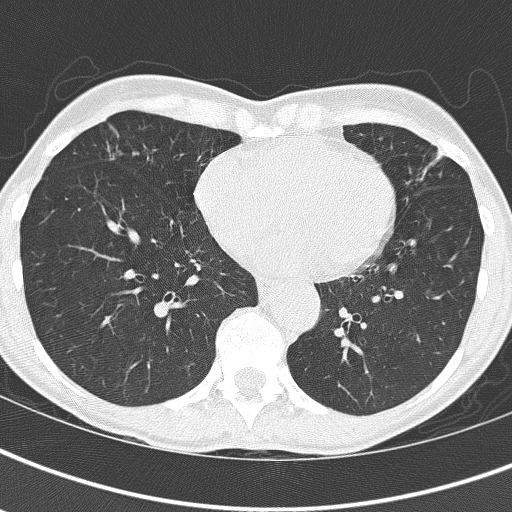
Axial slice from a low-dose chest CT screening exam; first (baseline) screen; lung window (W 1500 / L -600 HU); 2 mm slice thickness; slice 103 of 161 in the series. Female participant, aged 67 years at enrolment. Current smoker at enrolment.
- Lesion marked by an expert reader, bounding box [x1, y1, x2, y2] px = [81, 115, 180, 199].
- No non-calcified nodule or mass ≥4 mm was recorded by the screening reader at this exam.
- Official screen result: negative screen, significant abnormalities not suspicious for lung cancer.
- Later outcome: lung cancer diagnosed 832 days after this screen — bronchiolo-alveolar adenocarcinoma, NOS, right middle lobe, well differentiated (G1), stage IA (AJCC 6th edition), 25 mm at pathology.